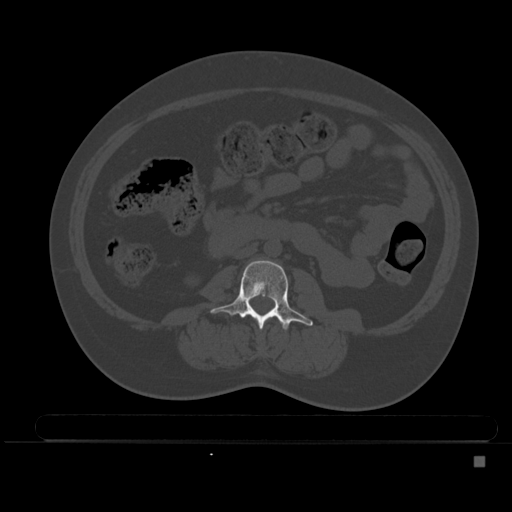
CT including the spine, one axial slice. Position 153 of 495 along the scan axis. Bone window (W 1800 / L 400 HU). 512 × 512 image matrix, field of view 404 × 404 mm. Patient: female, 33 years. From the clinical record (not read from this slice): primary cancer: breast; vertebrae with lytic lesions (as recorded): T1.
Outlined on this slice (semi-automatically segmented with operator editing):
- L2 vertebra: bounding box (x1, y1, x2, y2) in pixels: (278, 319, 280, 322)
- L3 vertebra: (210, 260, 313, 331)